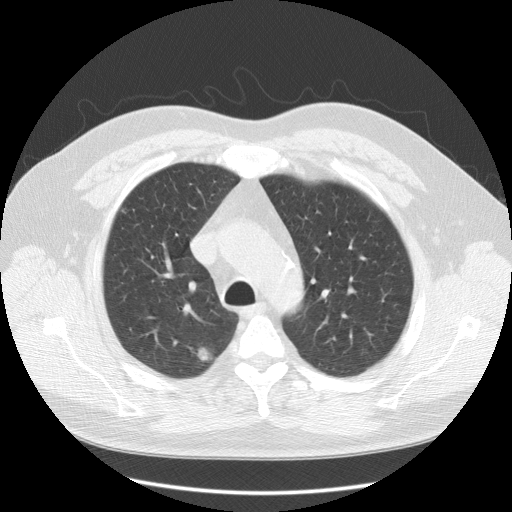
Chest CT (low-dose screening protocol), one axial image; baseline screening round; lung window (W 1500 / L -600 HU); 120 kVp. Male, age 55 years at enrolment. Former smoker at enrolment.
Lesion marked by an expert reader, bounding box <184,332,232,375> (left, top, right, bottom; pixels). The screening reader recorded 2 non-calcified nodules or masses ≥4 mm on this exam (right upper lobe, left upper lobe); which of them this box marks is not recorded. Lung cancer was diagnosed 84 days after this screen: large cell neuroendocrine carcinoma, right upper lobe, poorly differentiated (G3), stage IA (AJCC 6th edition), 18 mm at pathology.